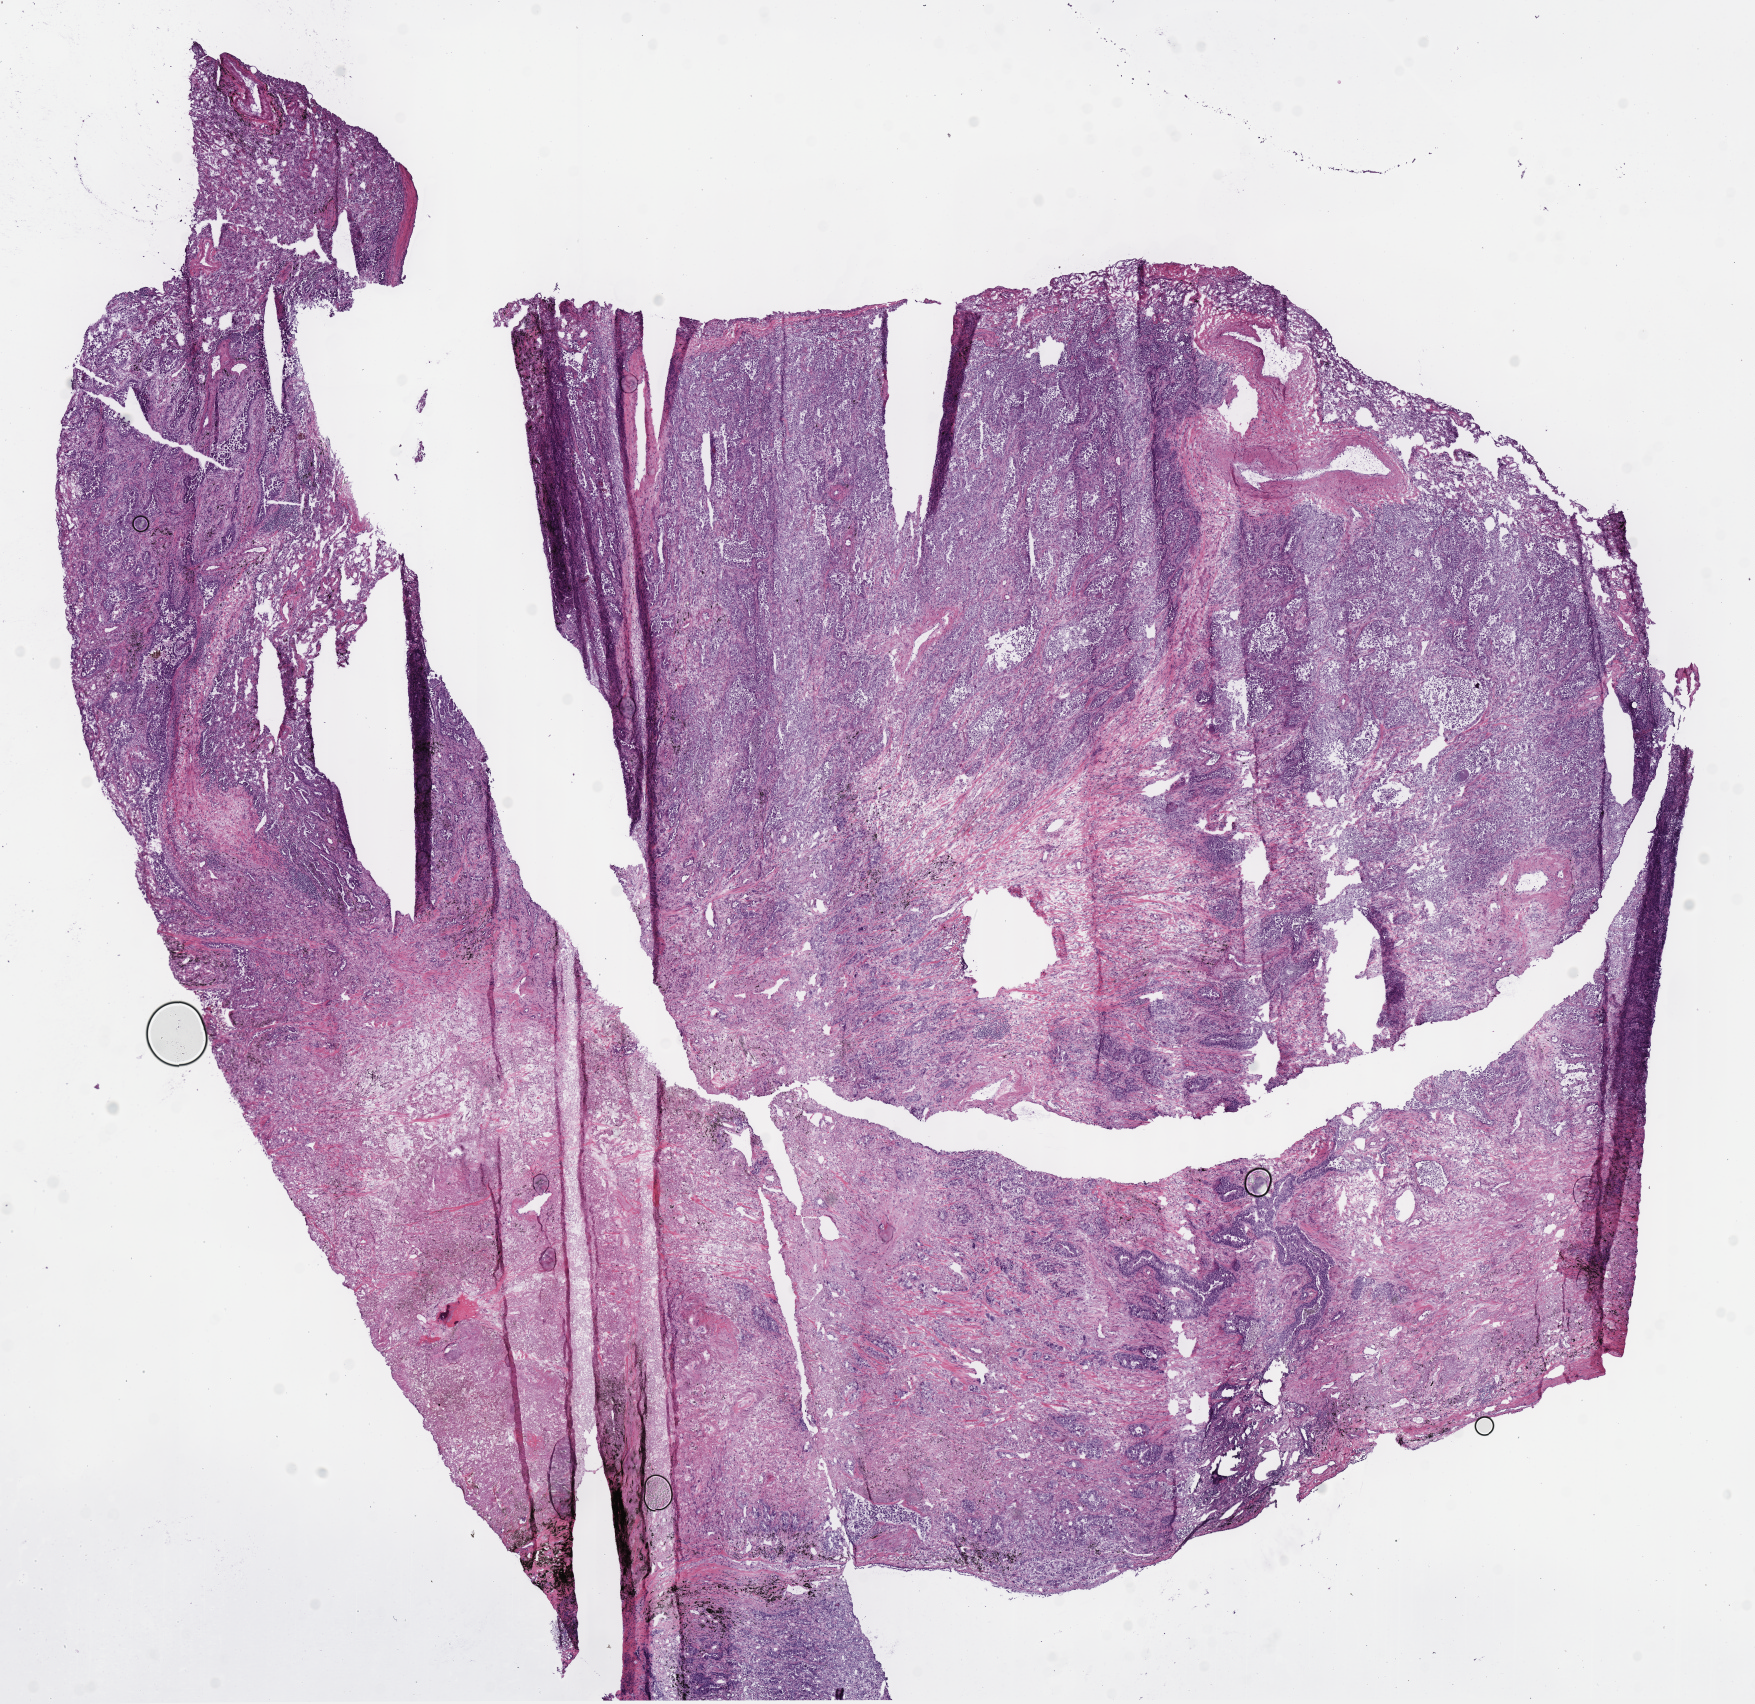
H&E-stained whole-slide image, whole scanned area (about 13.8 x 13.4 mm, from a 40x scan) shown as a low-resolution overview. Frozen section from the bottom of the tissue portion. Lung, primary tumour sample. Patient: male, age at initial diagnosis 58 years. Pathologist review of this section (percent, as recorded): tumour cells 83%, tumour nuclei 80%, normal cells 3%, stromal cells 14%, necrosis 0%. Inflammatory infiltration, as recorded: lymphocyte infiltration 5%, monocyte infiltration 5%, neutrophil infiltration 0%.
Pathologic diagnosis: Bronchiolo-alveolar adenocarcinoma, NOS (upper lobe, lung). AJCC pathologic stage: IB. TNM: T2a N0 M0.